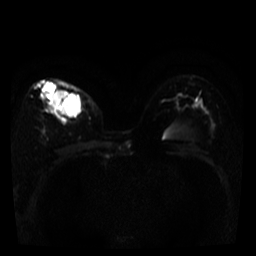
Breast MRI, one axial slice; position 24 of 39 along the scan axis; diffusion-weighted series; image 2 of 4 stored at this slice position (different b-values; order by instance number); 3 T; 5 mm slice thickness; 256 × 256 image matrix, field of view 280 × 280 mm. Female patient.
Structures marked on this image (manually delineated by an expert):
- tumour on diffusion-weighted imaging: bounding box <39,81,80,116> (left, top, right, bottom; pixels)